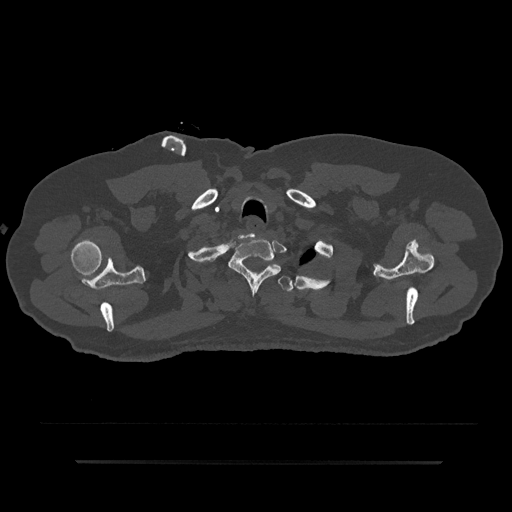
CT including the spine, one axial slice; slice 730 of 797 in the series (ordered by position); reconstruction kernel Br40s/3; bone window (W 1800 / L 400 HU); 0.5 mm slice thickness; 512 × 512 image matrix, field of view 464 × 464 mm. Patient: male, 59 years. From the clinical record (not read from this slice): primary cancer: bile ducts.
Annotated regions visible in this slice (semi-automatically segmented with operator editing):
- T1 vertebra: bounding box <229,234,281,294> (left, top, right, bottom; pixels)
- T2 vertebra: <220,264,293,292>